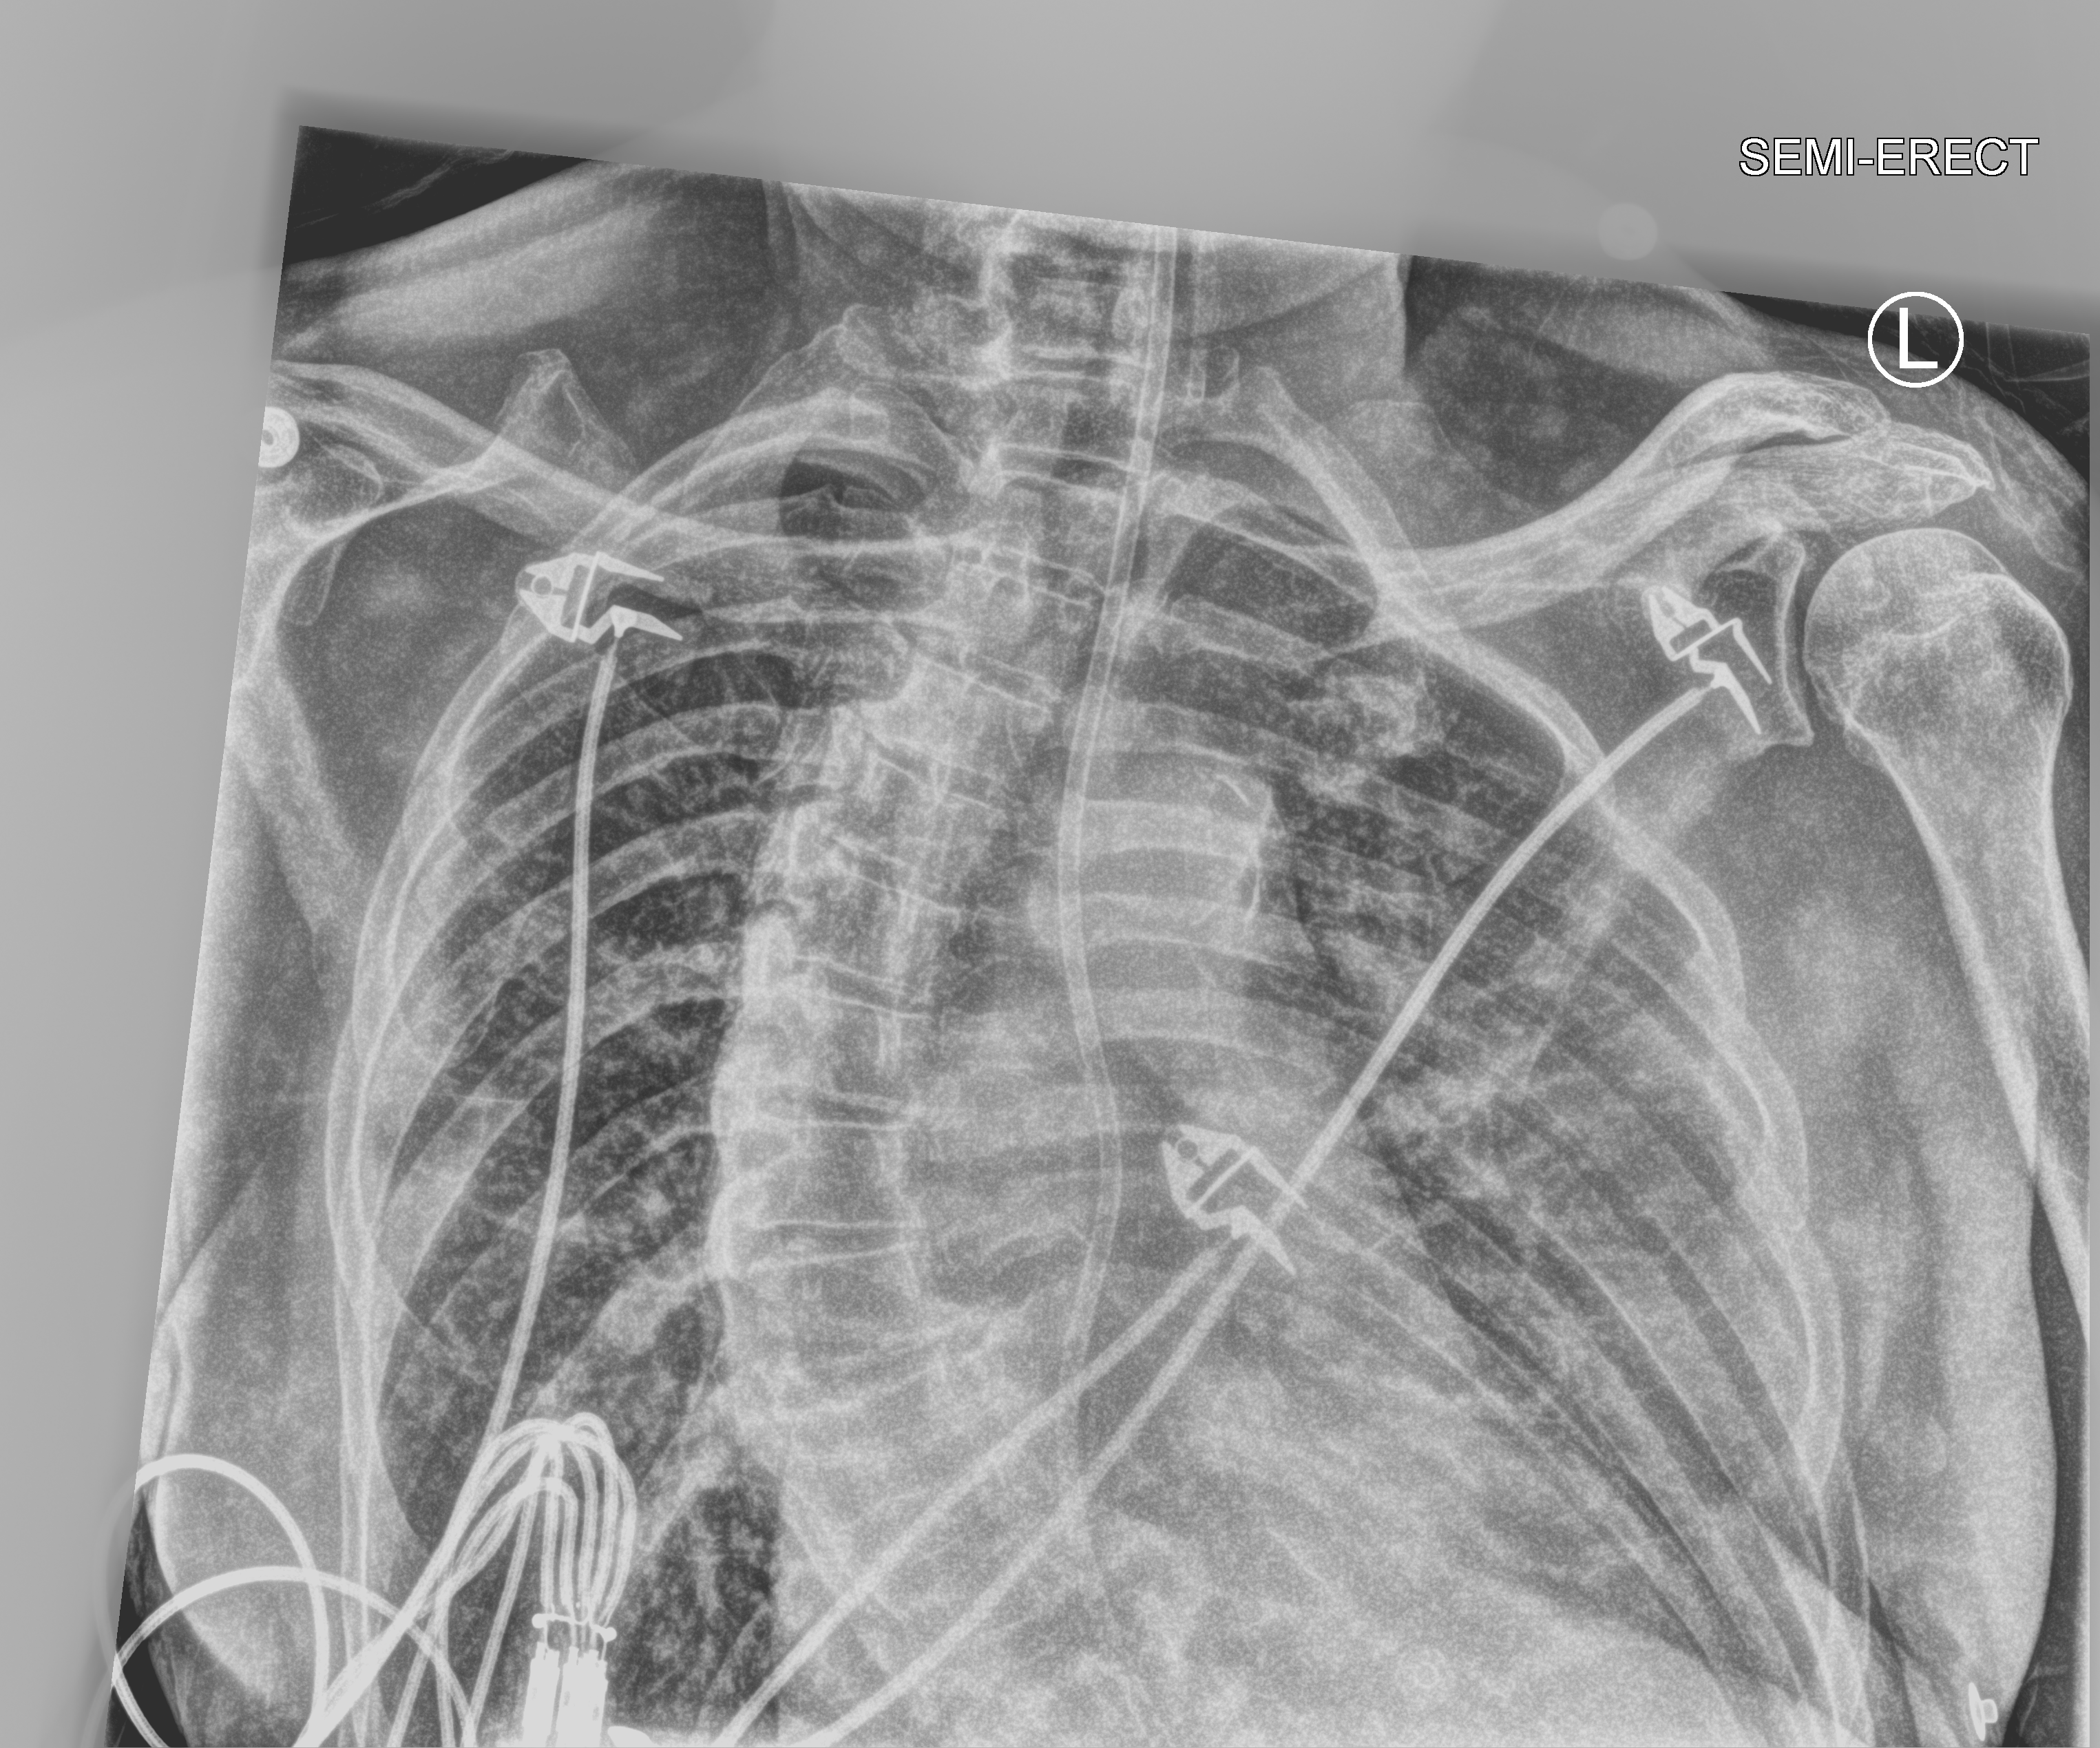
Bedside chest radiograph (computed radiography); anteroposterior (AP) projection. Male patient hospitalised with COVID-19, age 75–90 years.
Hospital-stay facts (about this admission, not read from this image; timing relative to this image not recorded): admitted to intensive care during this hospital stay: no; length of hospital stay: 12 days.